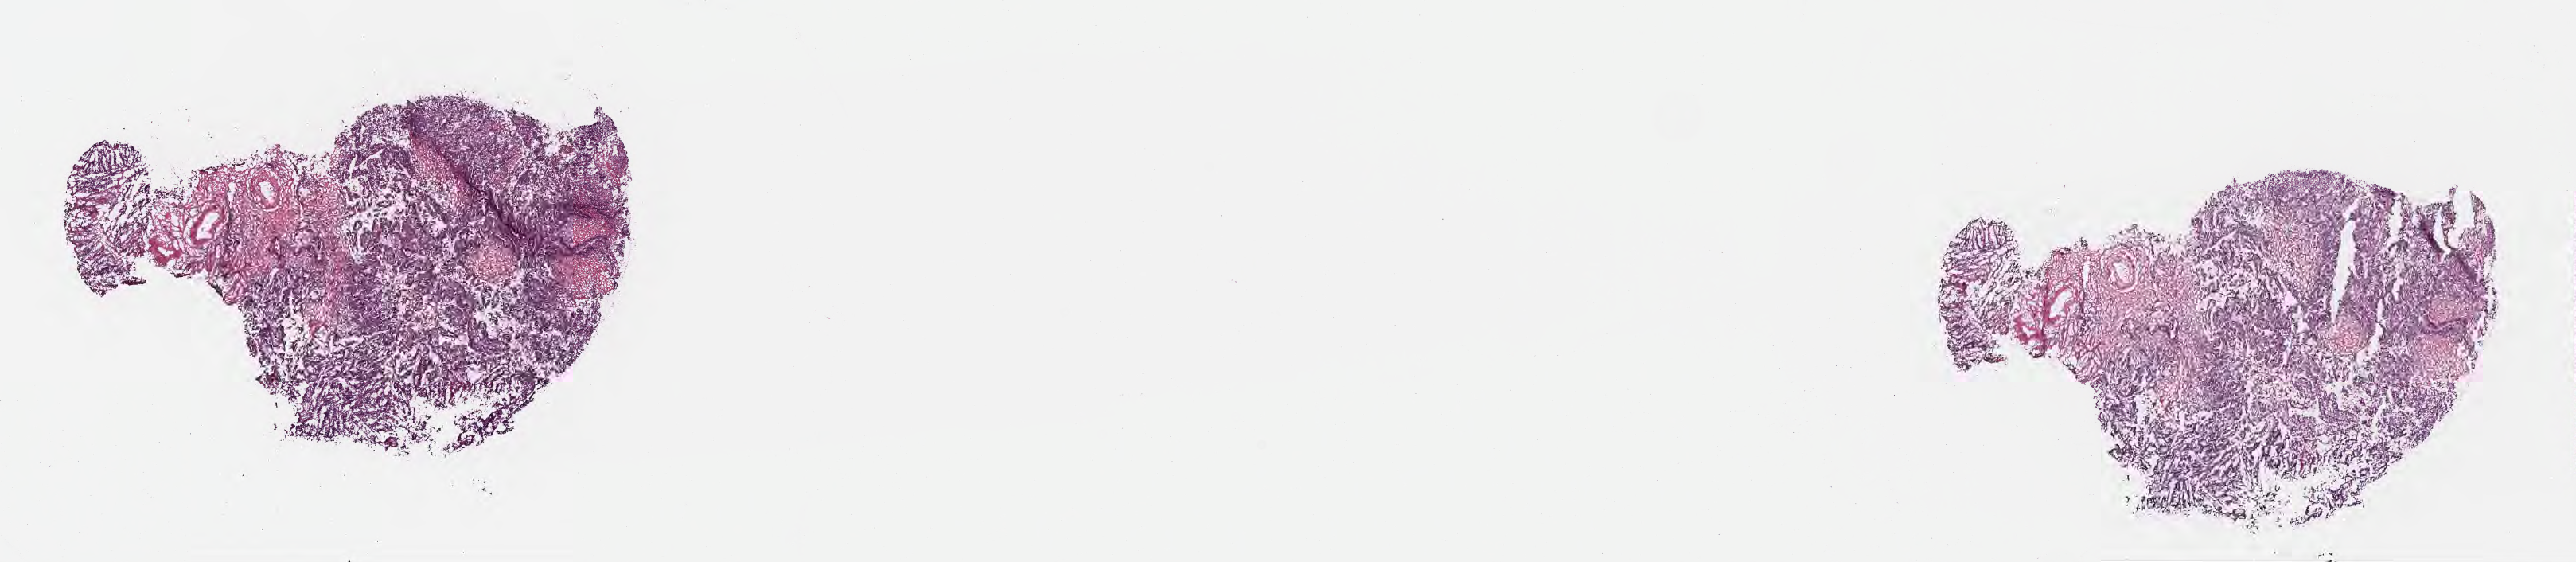
Haematoxylin and eosin whole-slide image, shown as a low-resolution overview of the whole scanned area (about 26.2 x 5.7 mm); frozen section; primary tumor; anatomic site: sigmoid colon. Female, age 55 years at initial diagnosis. Slide review estimates, as recorded: tumor cells 80%, tumor nuclei 80%, stromal cells 15%, necrosis 1%, normal cells 4%. Inflammatory infiltration, as recorded: lymphocyte infiltration 3%, monocyte infiltration 2%, neutrophil infiltration 6%.
Histologic diagnosis: Adenocarcinoma, NOS.